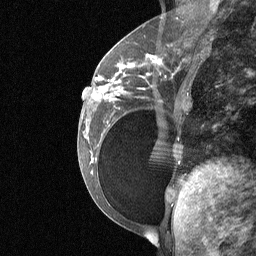
Breast MRI (dynamic contrast-enhanced), one sagittal slice; slice 25 of 64 in the series (ordered by position); dynamic contrast-enhanced study with each time point stored as its own series, time point 2 of 3 at this slice position (early post-contrast, ordered by acquisition time); 1.5 T; TE 4.8 ms, TR 27 ms; 2 mm slice thickness; 256 × 256 image matrix. Female patient, age 34 years. From the clinical record (not read from this slice): setting: breast cancer imaged before/during neoadjuvant chemotherapy; receptor status: HR-positive, HER2-negative.
Structures marked on this image (semi-automatic segmentation, software-assisted and operator-edited):
- analysis volume of interest (the breast-tissue region the enhancement analysis was run in; not a lesion): bounding box (x1, y1, x2, y2) in pixels: (92, 50, 188, 185)
- tumour enhancement mask (voxels above the 90 % enhancement threshold inside the analysis volume of interest): (96, 54, 160, 100)